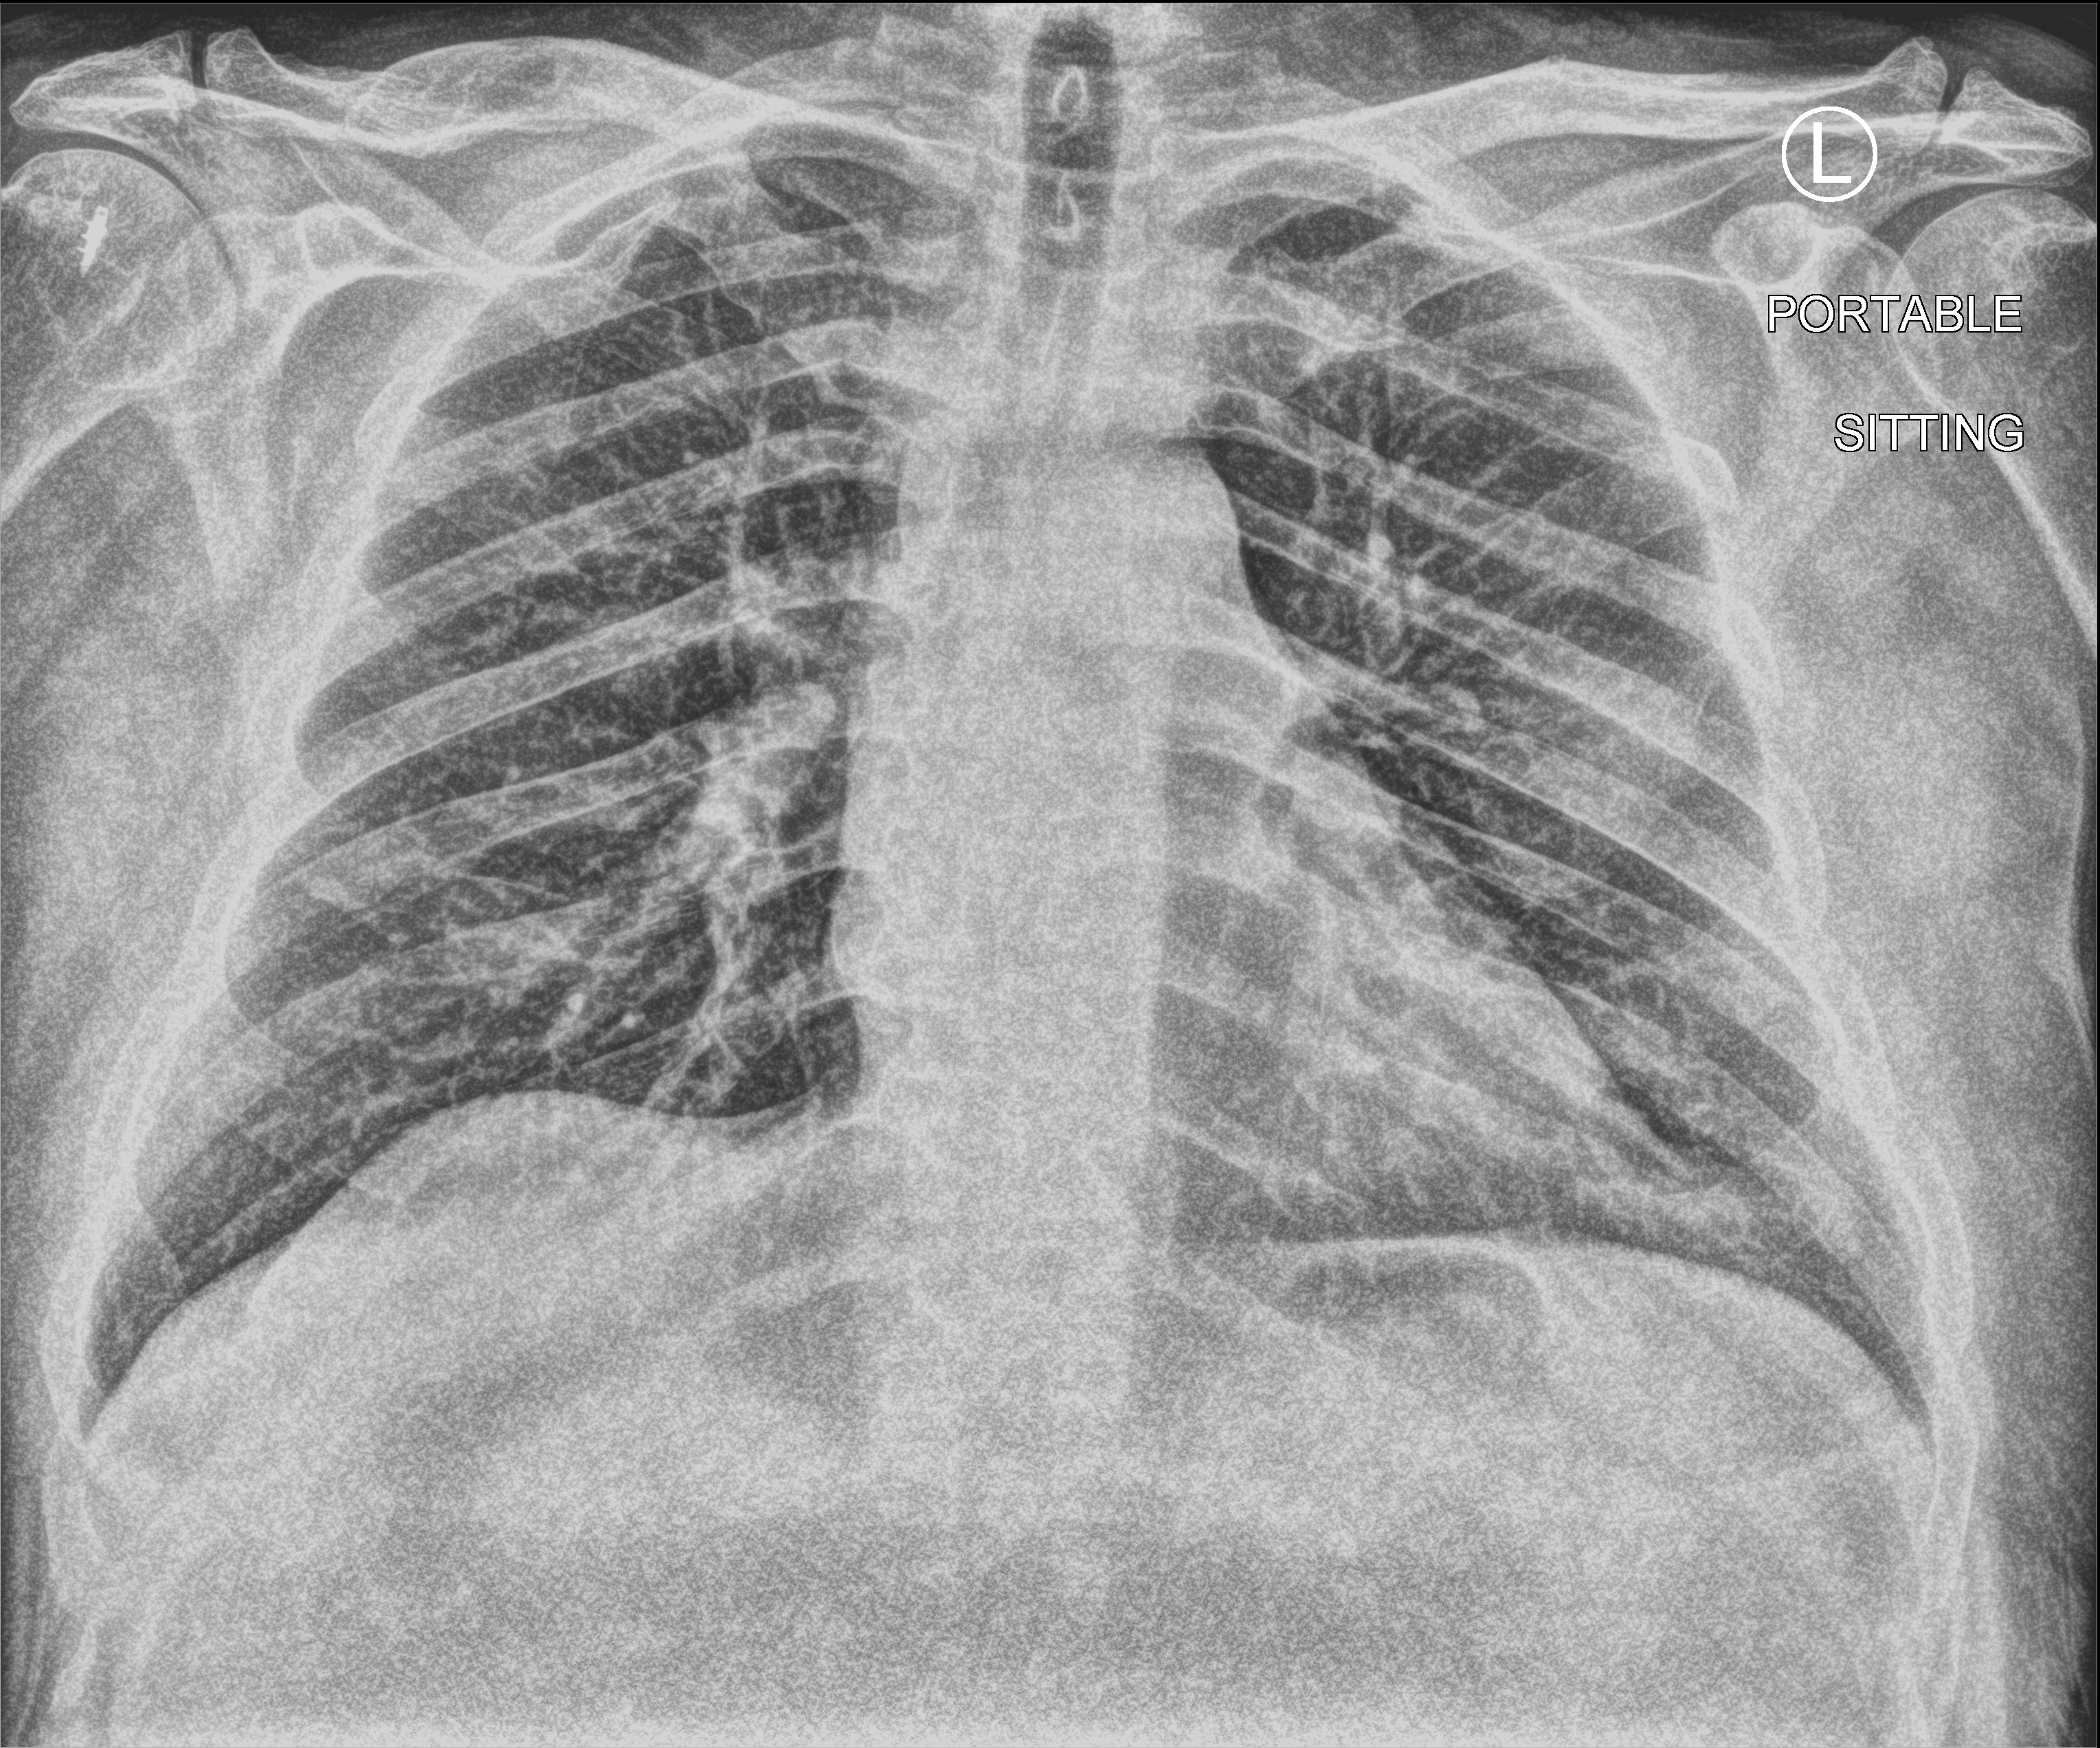
Chest X-ray (portable). Male patient hospitalised with COVID-19, age 60–74 years.
Hospital-stay facts (about this admission, not read from this image; timing relative to this image not recorded):
- mechanically ventilated during this hospital stay: no
- hypertension (admission record): yes
- length of hospital stay: 3 days